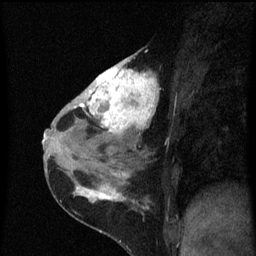
Breast MRI (dynamic contrast-enhanced), one sagittal slice. Position 32 of 60 along the scan axis. Dynamic contrast-enhanced series, image 2 of 3 at this slice position (ordered by acquisition). 1.5 T. TE 4.2 ms, TR 8 ms. 2 mm slice thickness. 256 × 256 image matrix, field of view 180 × 180 mm. Patient: female, 38 years.
Outlined on this slice (semi-automatic segmentation, software-assisted and operator-edited):
- analysis volume of interest (the breast-tissue region the enhancement analysis was run in; not a lesion): bounding box <80,52,159,151> (left, top, right, bottom; pixels)
- tumour enhancement mask (voxels above the 70 % enhancement threshold inside the analysis volume of interest): <80,58,159,137>